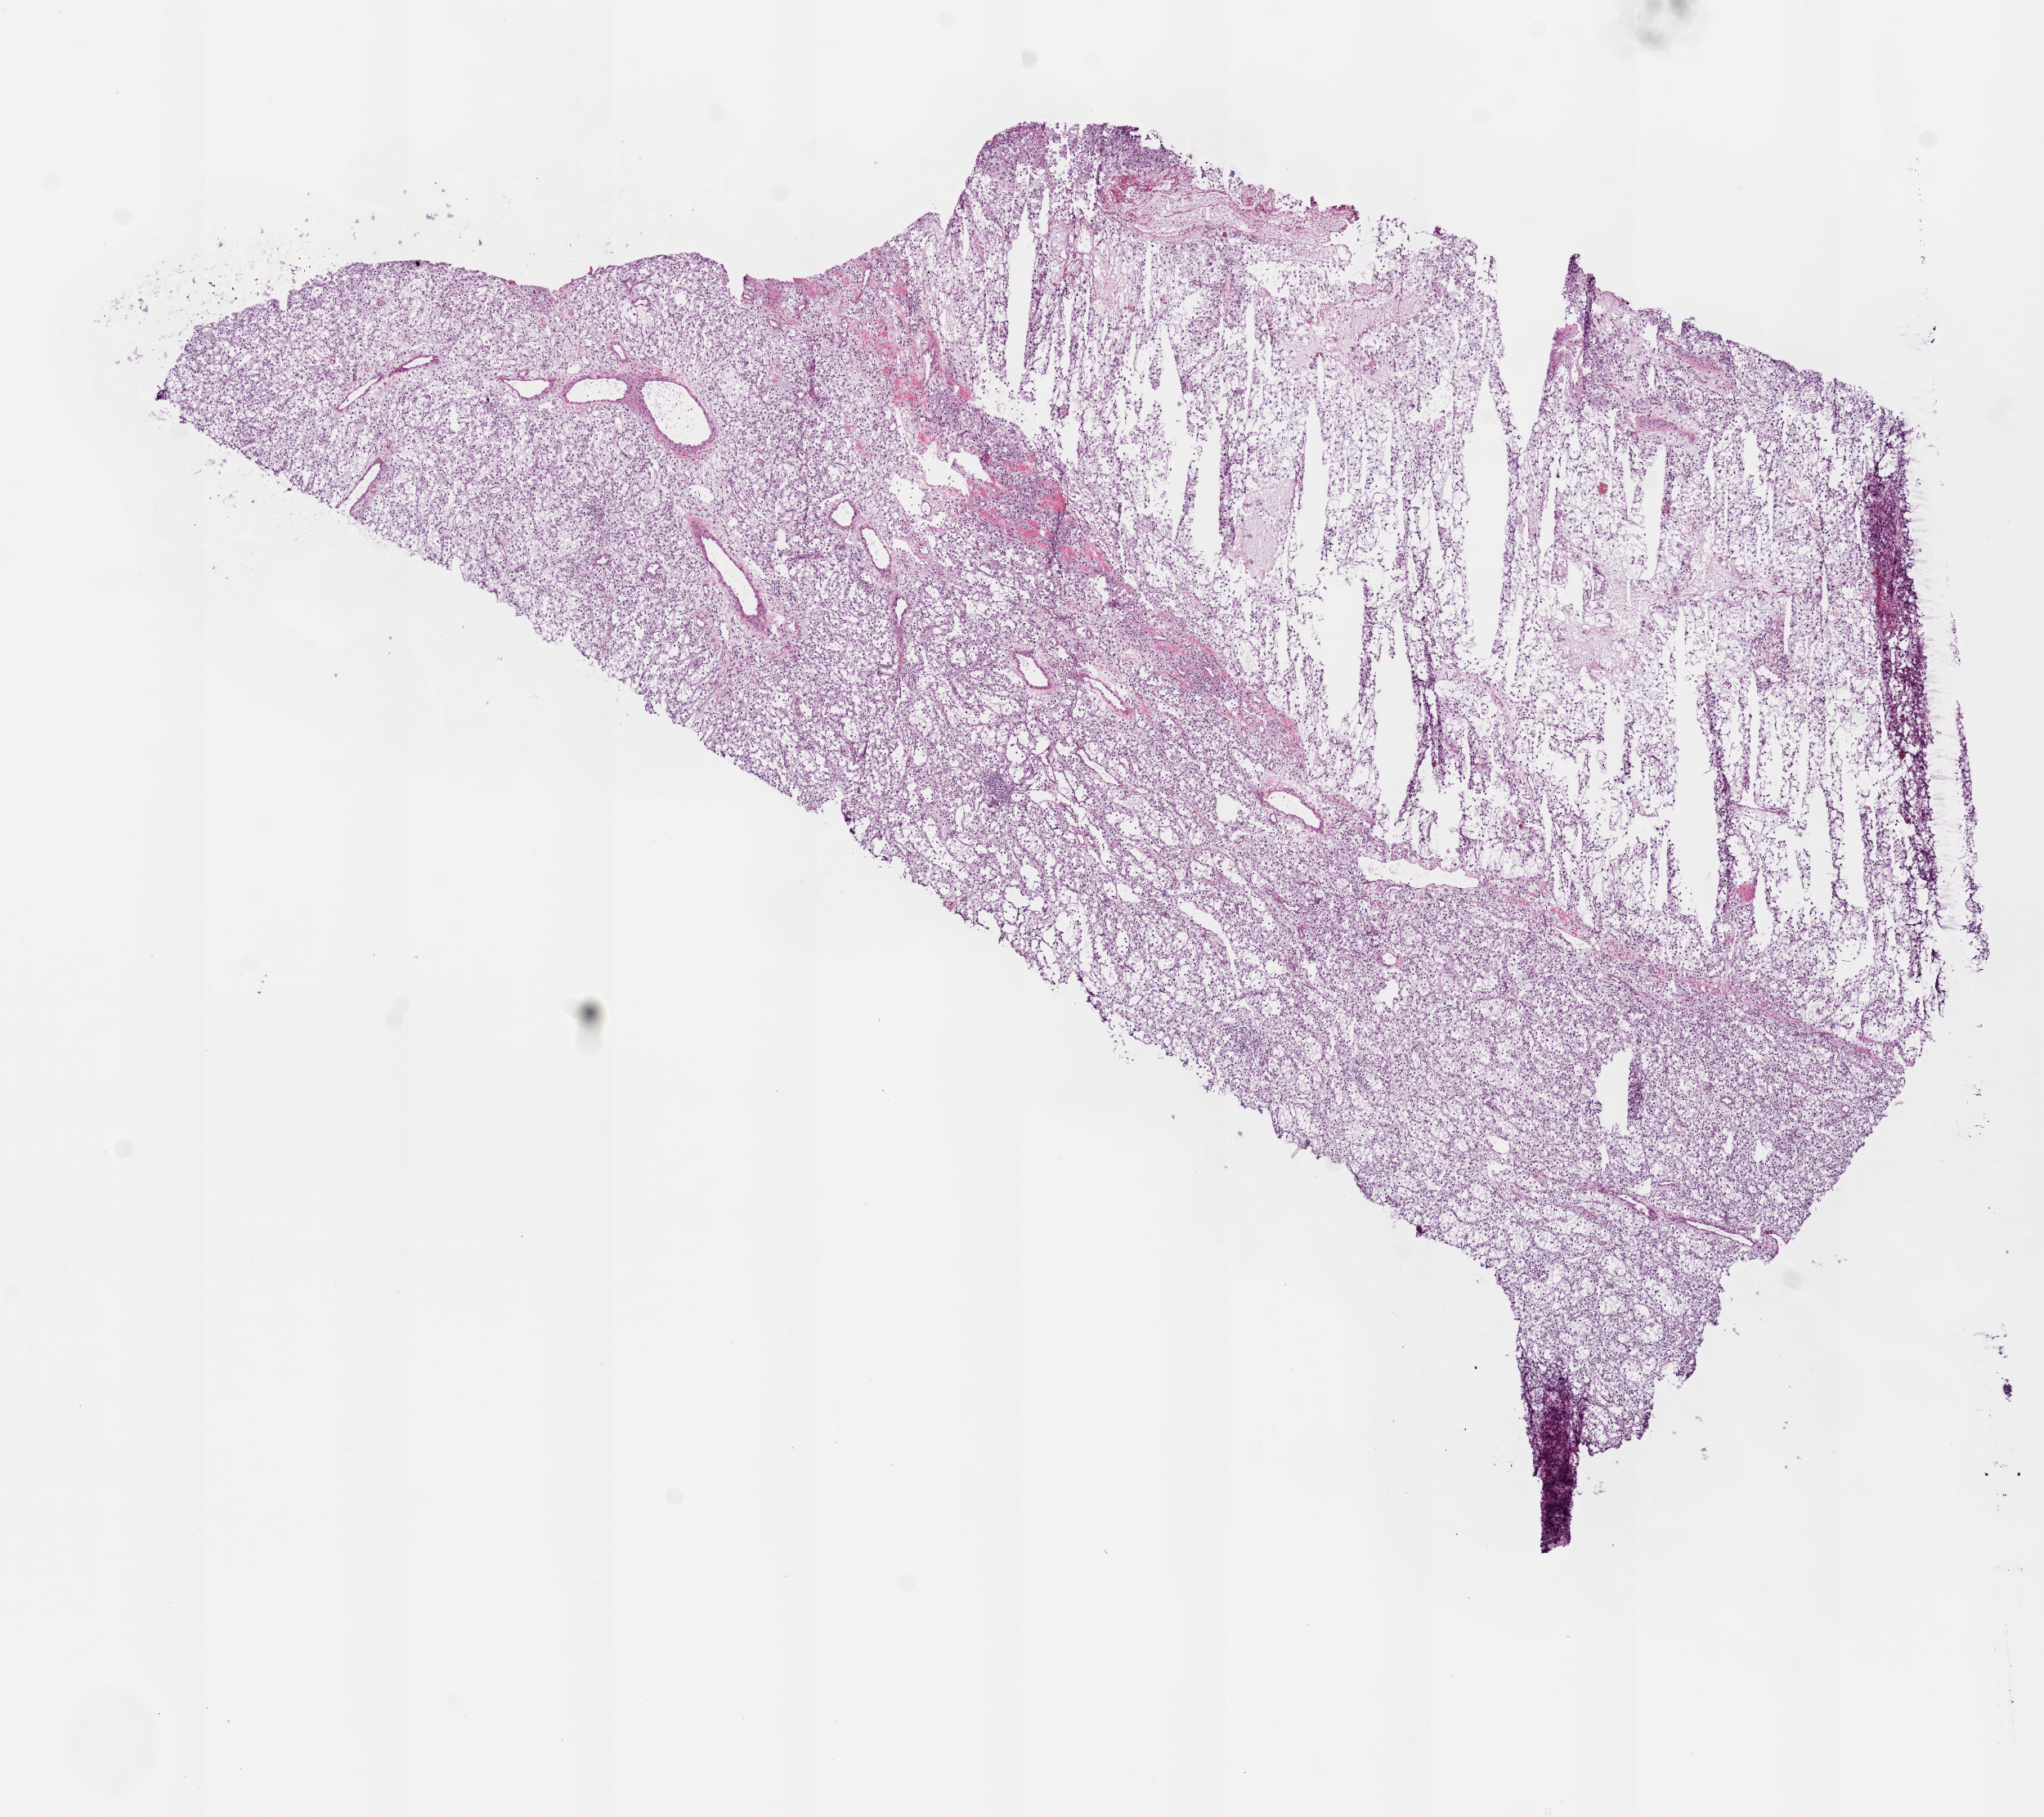
H&E whole-slide image, shown as a low-resolution overview of the whole scanned area (about 10.0 x 8.9 mm, from a 20x scan), frozen section from the top of the tissue portion, primary tumour sample from the kidney. Female, age 78 years at initial diagnosis. Histologic grade: G2 (moderately differentiated). Pathologist review of this section (percent, as recorded): tumour cells 90%, tumour nuclei 85%, normal cells 0%, stromal cells 10%, necrosis 0%.
- AJCC pathologic stage: I
- histologic diagnosis: Clear cell adenocarcinoma, NOS
- TNM: T1a NX M0
- laterality: right